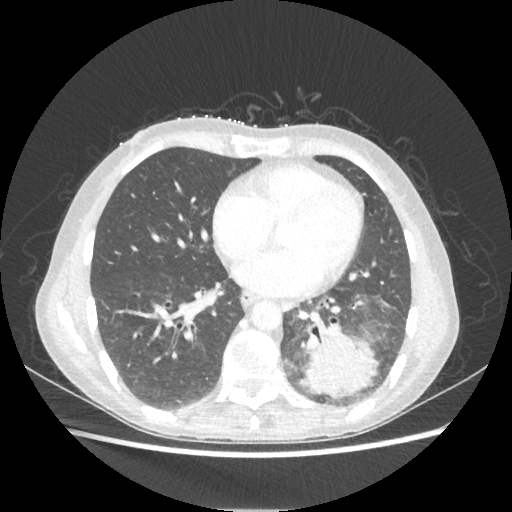
Chest CT, one axial slice; slice 91 of 221 in the series (ordered by position); lung window (W 1500 / L -600 HU); 512 × 512 image matrix, field of view 360 × 360 mm. Female patient, age 53 years. From the clinical record (not read from this slice): clinical TNM (as recorded): T3 N0 M0.
Annotated regions visible in this slice (bounding box drawn by a radiologist):
- lung tumour (recorded histology: adenocarcinoma): box from (x=301, y=318) to (x=378, y=399) px